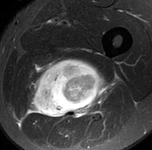
MRI of an extremity soft-tissue mass, one axial slice. Slice 77 of 90 in the series (ordered by position). STIR. MR volume resampled by the dataset authors to the PET/CT grid (not the native acquisition matrix). 3.27 mm slice thickness. 152 × 150 image matrix, field of view 148 × 146 mm. Male patient. Case-level facts recorded for this patient, not image findings: histological type: undifferentiated pleomorphic liposarcoma; grade: high; site of the primary tumour: left thigh.
Structures marked on this image (expert contour drawn on MRI and transferred to this co-registered scan by the dataset authors):
- gross tumour volume including surrounding oedema: box from (x=25, y=55) to (x=113, y=124) px
- gross tumour volume (mass): (x=34, y=59)–(x=110, y=117)